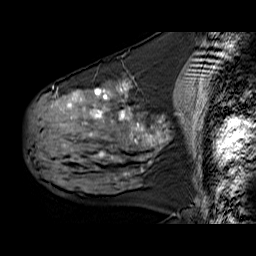
Breast MRI (dynamic contrast-enhanced), one sagittal slice. Slice 28 of 60 in the series (ordered by position). Dynamic contrast-enhanced series, time point 2 of 6 at this slice position (early post-contrast). 1.5 T. TE 6.3 ms, TR 32.9 ms. 4 mm slice thickness. 256 × 256 image matrix, field of view 200 × 200 mm. Female patient. From the clinical record (not read from this slice): setting: breast cancer imaged before/during neoadjuvant chemotherapy; receptor status: HER2-positive.
Outlined on this slice (semi-automatic segmentation, software-assisted and operator-edited):
- analysis volume of interest (the breast-tissue region the enhancement analysis was run in; not a lesion): box from (x=30, y=78) to (x=168, y=180) px
- tumour enhancement mask (voxels above the 100 % enhancement threshold inside the analysis volume of interest): (x=67, y=82)–(x=160, y=171)